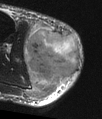
MRI of an extremity soft-tissue mass, one axial slice. Position 22 of 48 along the scan axis. T2-weighted fat-saturated. MR volume resampled by the dataset authors to the PET/CT grid (not the native acquisition matrix). 3.27 mm slice thickness. 102 × 119 image matrix, field of view 100 × 116 mm. Male patient. From the clinical record (not read from this slice): histological type: pleiomorphic liposarcoma; grade: high; site of the primary tumour: right calf.
Outlined on this slice (expert contour drawn on MRI and transferred to this co-registered scan by the dataset authors):
- gross tumour volume including surrounding oedema: bounding box (x1, y1, x2, y2) in pixels: (25, 23, 81, 100)
- gross tumour volume (mass): (26, 28, 81, 84)